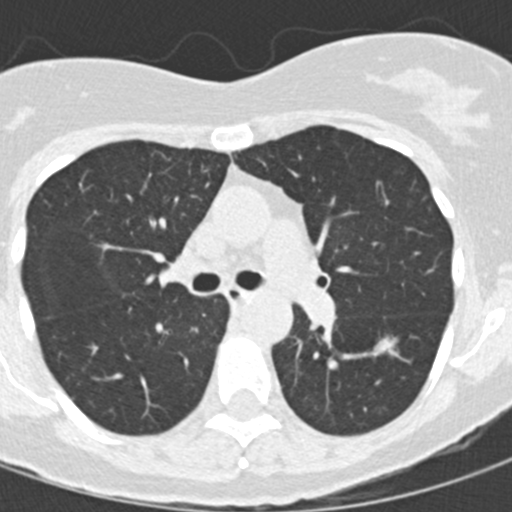
Low-dose screening chest CT, one axial slice; reconstruction kernel B30f; lung window (W 1500 / L -600 HU); 2 mm slice thickness; 512 × 512 image matrix, field of view 270 × 270 mm.
Annotated regions visible in this slice (expert manual segmentation):
- lesion 1 (tumor, lower lobe of left lung): bounding box [x1, y1, x2, y2] px = [374, 337, 391, 352]